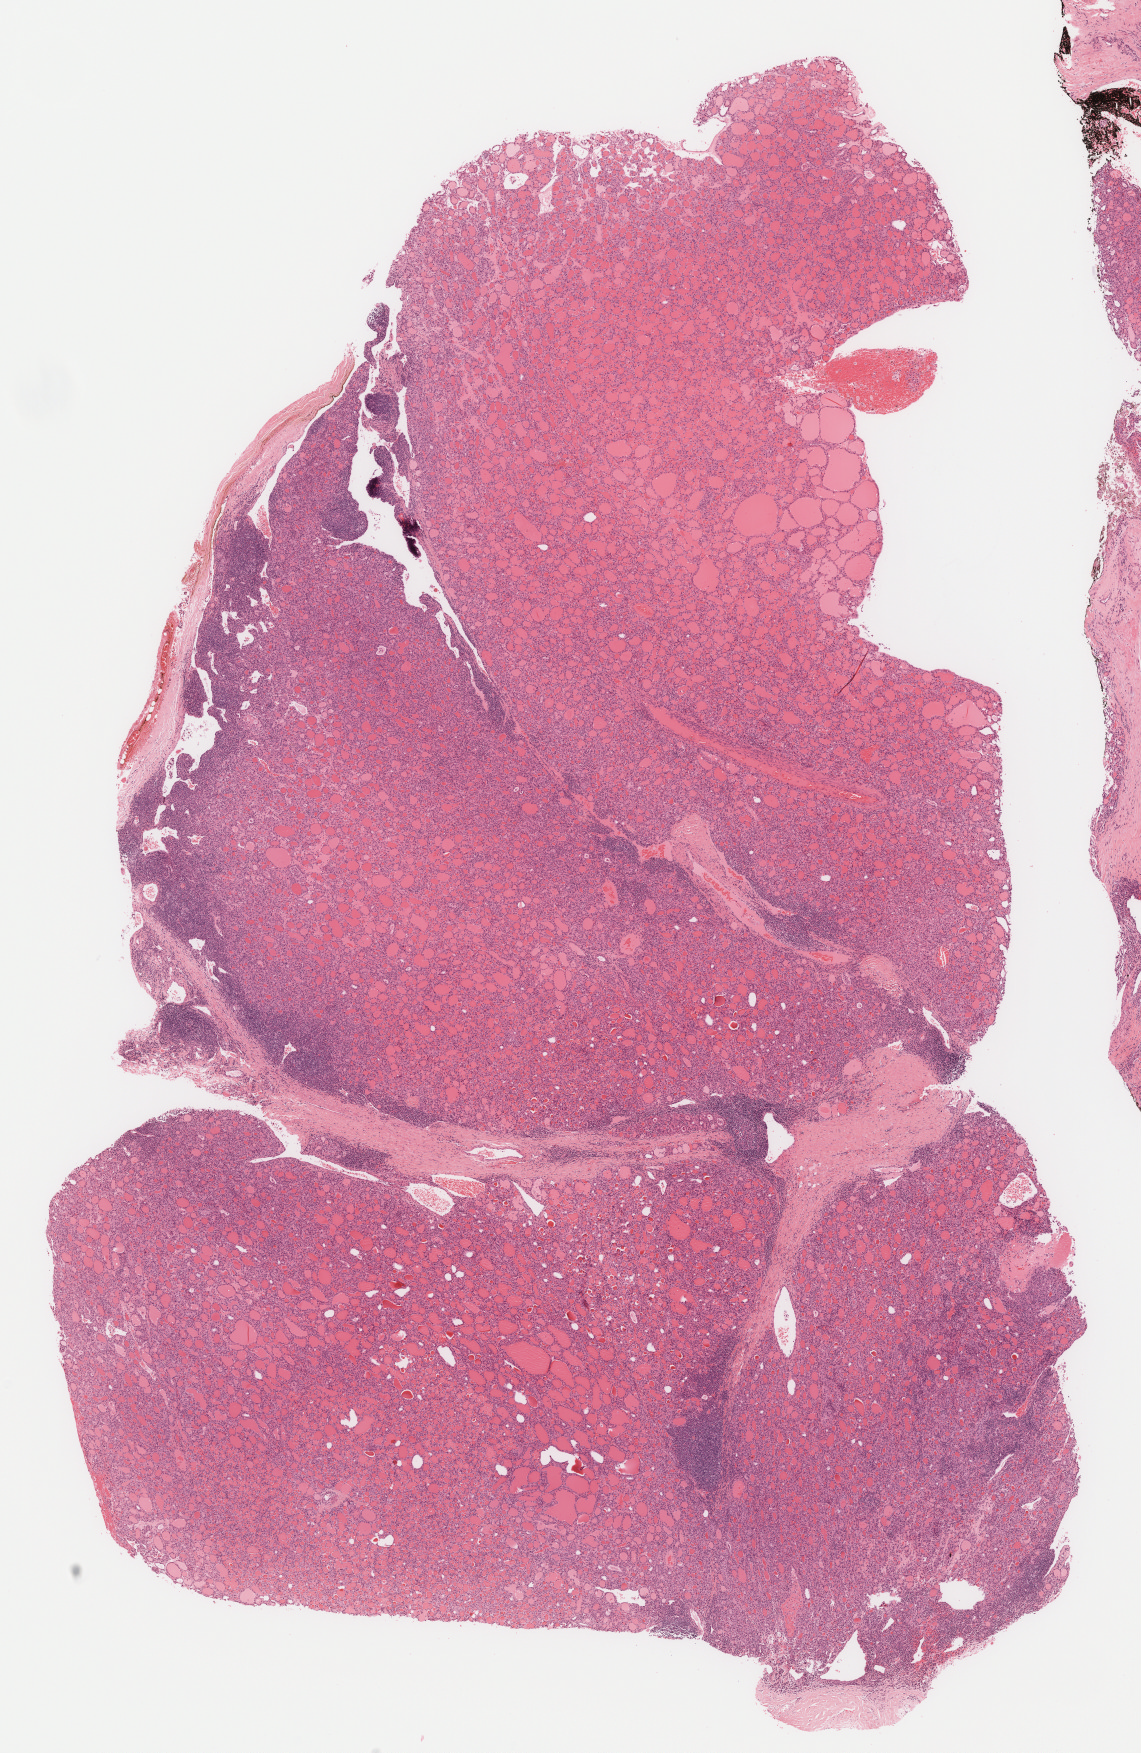
Hematoxylin and eosin (H&E) stained whole-slide image, shown as a low-resolution overview of the whole scanned area (about 9.2 x 14.1 mm); formalin-fixed paraffin-embedded (FFPE) diagnostic section; thyroid, primary tumour sample. Patient: male, age at initial diagnosis 39 years.
Lymph nodes positive (case pathology): 4 of 24 examined. AJCC pathologic stage: I (7th edition). Diagnosis: Papillary carcinoma, follicular variant (thyroid gland).